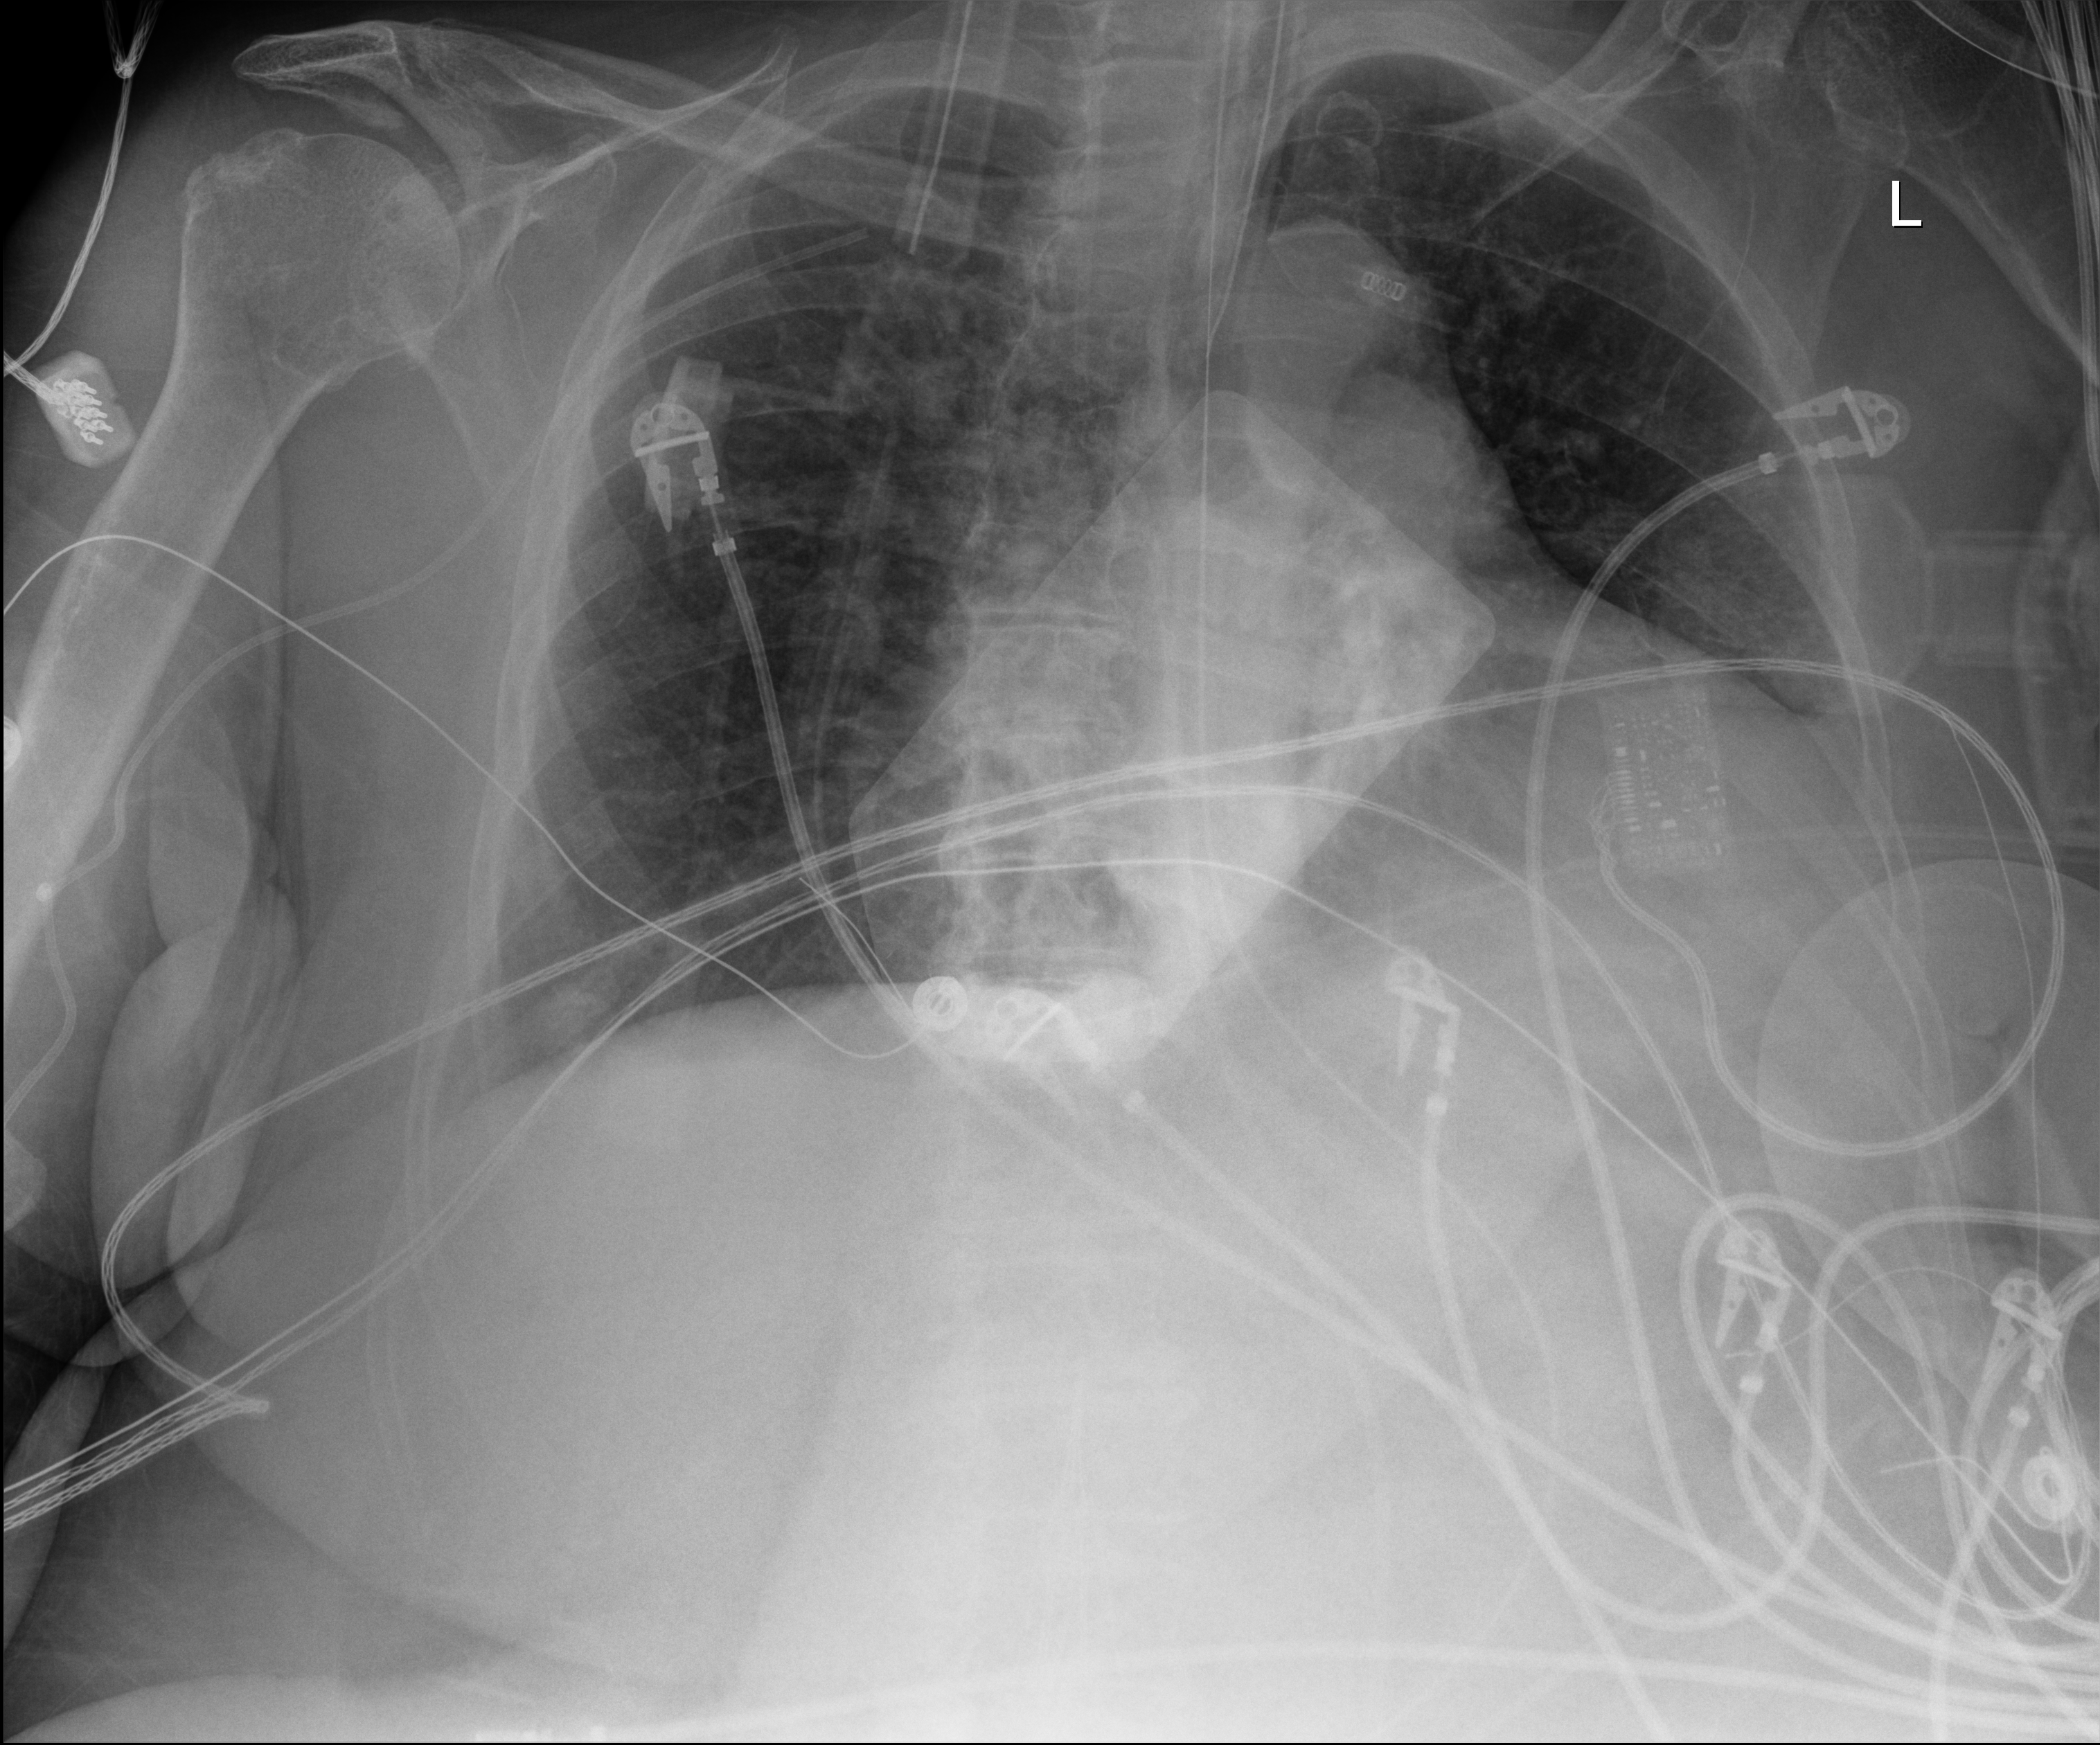
Portable chest radiograph, anteroposterior (AP) projection. Female patient hospitalised with COVID-19, age 75–90 years.
Admission-level facts for this patient (not findings on this image; timing relative to this image not recorded):
- mechanically ventilated during this hospital stay: yes
- chronic kidney disease (admission record): no
- admitted to intensive care during this hospital stay: yes